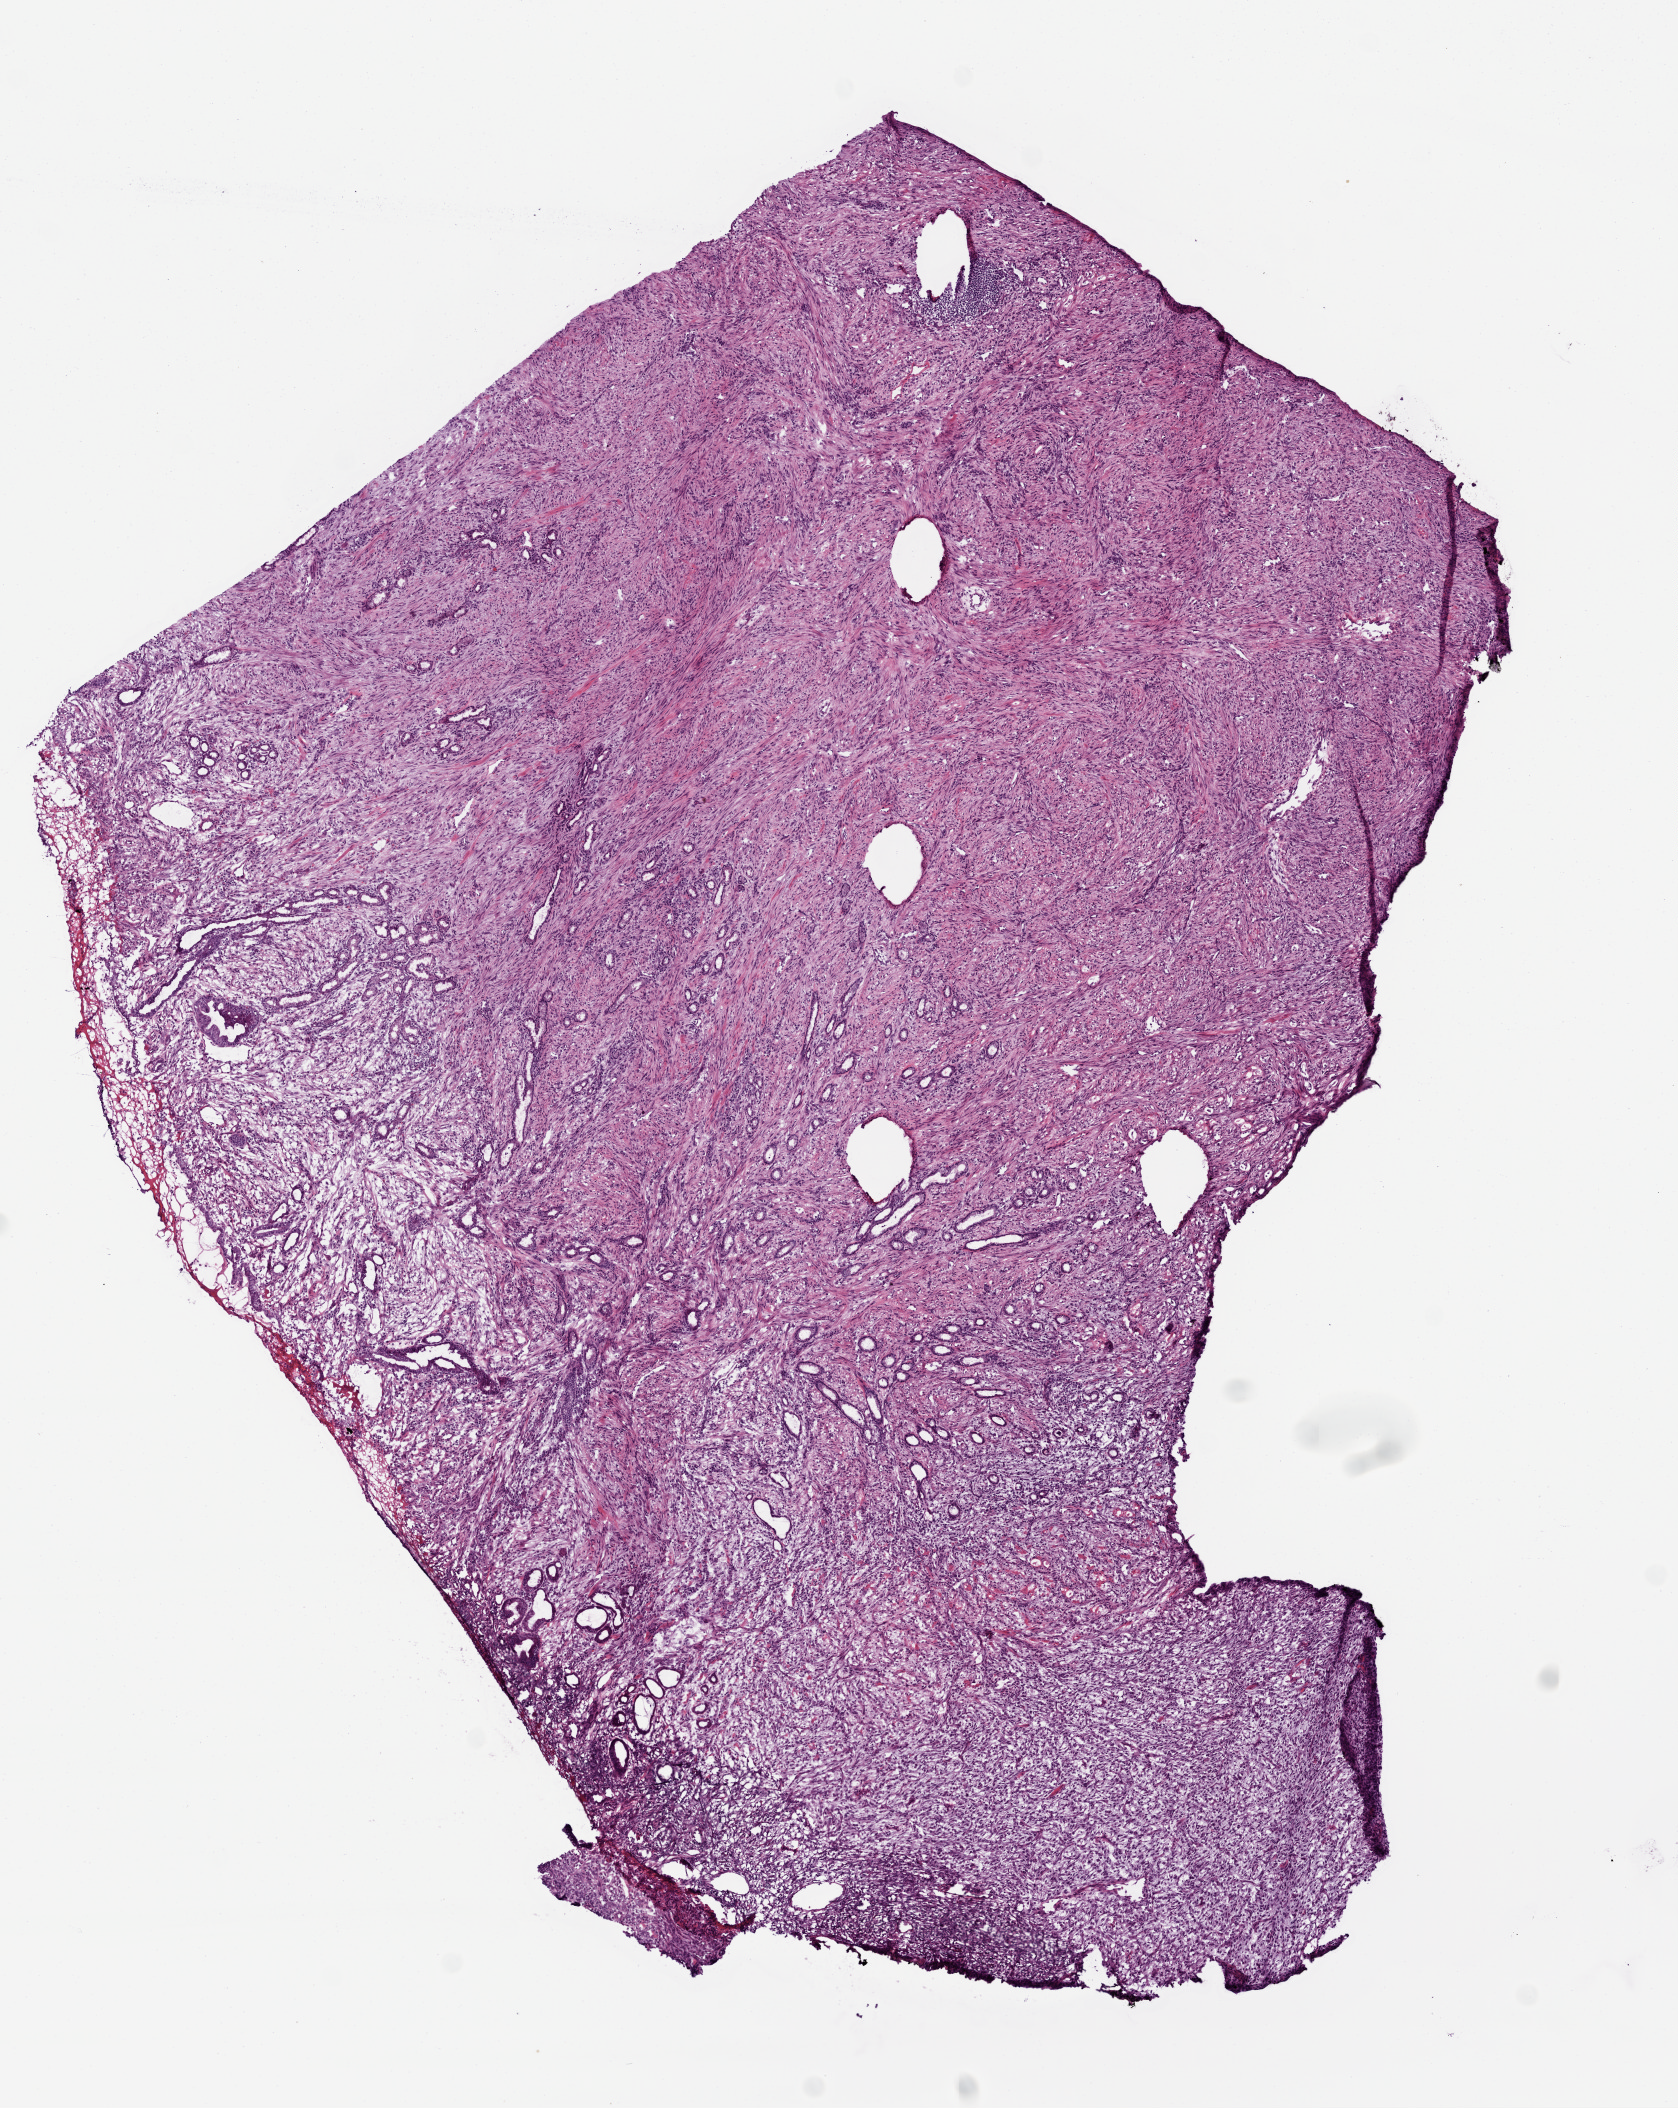
Digitized Hematoxylin and eosin (H&E) stained tissue section (whole slide) — low-resolution overview of the scanned area, about 6.8 x 8.5 mm; frozen section from the top of the tissue portion; primary tumour sample from the stomach. Patient: male, age at initial diagnosis 53 years. Pathologist review of this section (percent, as recorded): tumour cells 70%, tumour nuclei 70%, normal cells 5%, stromal cells 25%, necrosis 0%. Infiltration values recorded for this section: lymphocyte infiltration 0%, monocyte infiltration 0%, neutrophil infiltration 0%.
Pathologic diagnosis: Dedifferentiated liposarcoma.